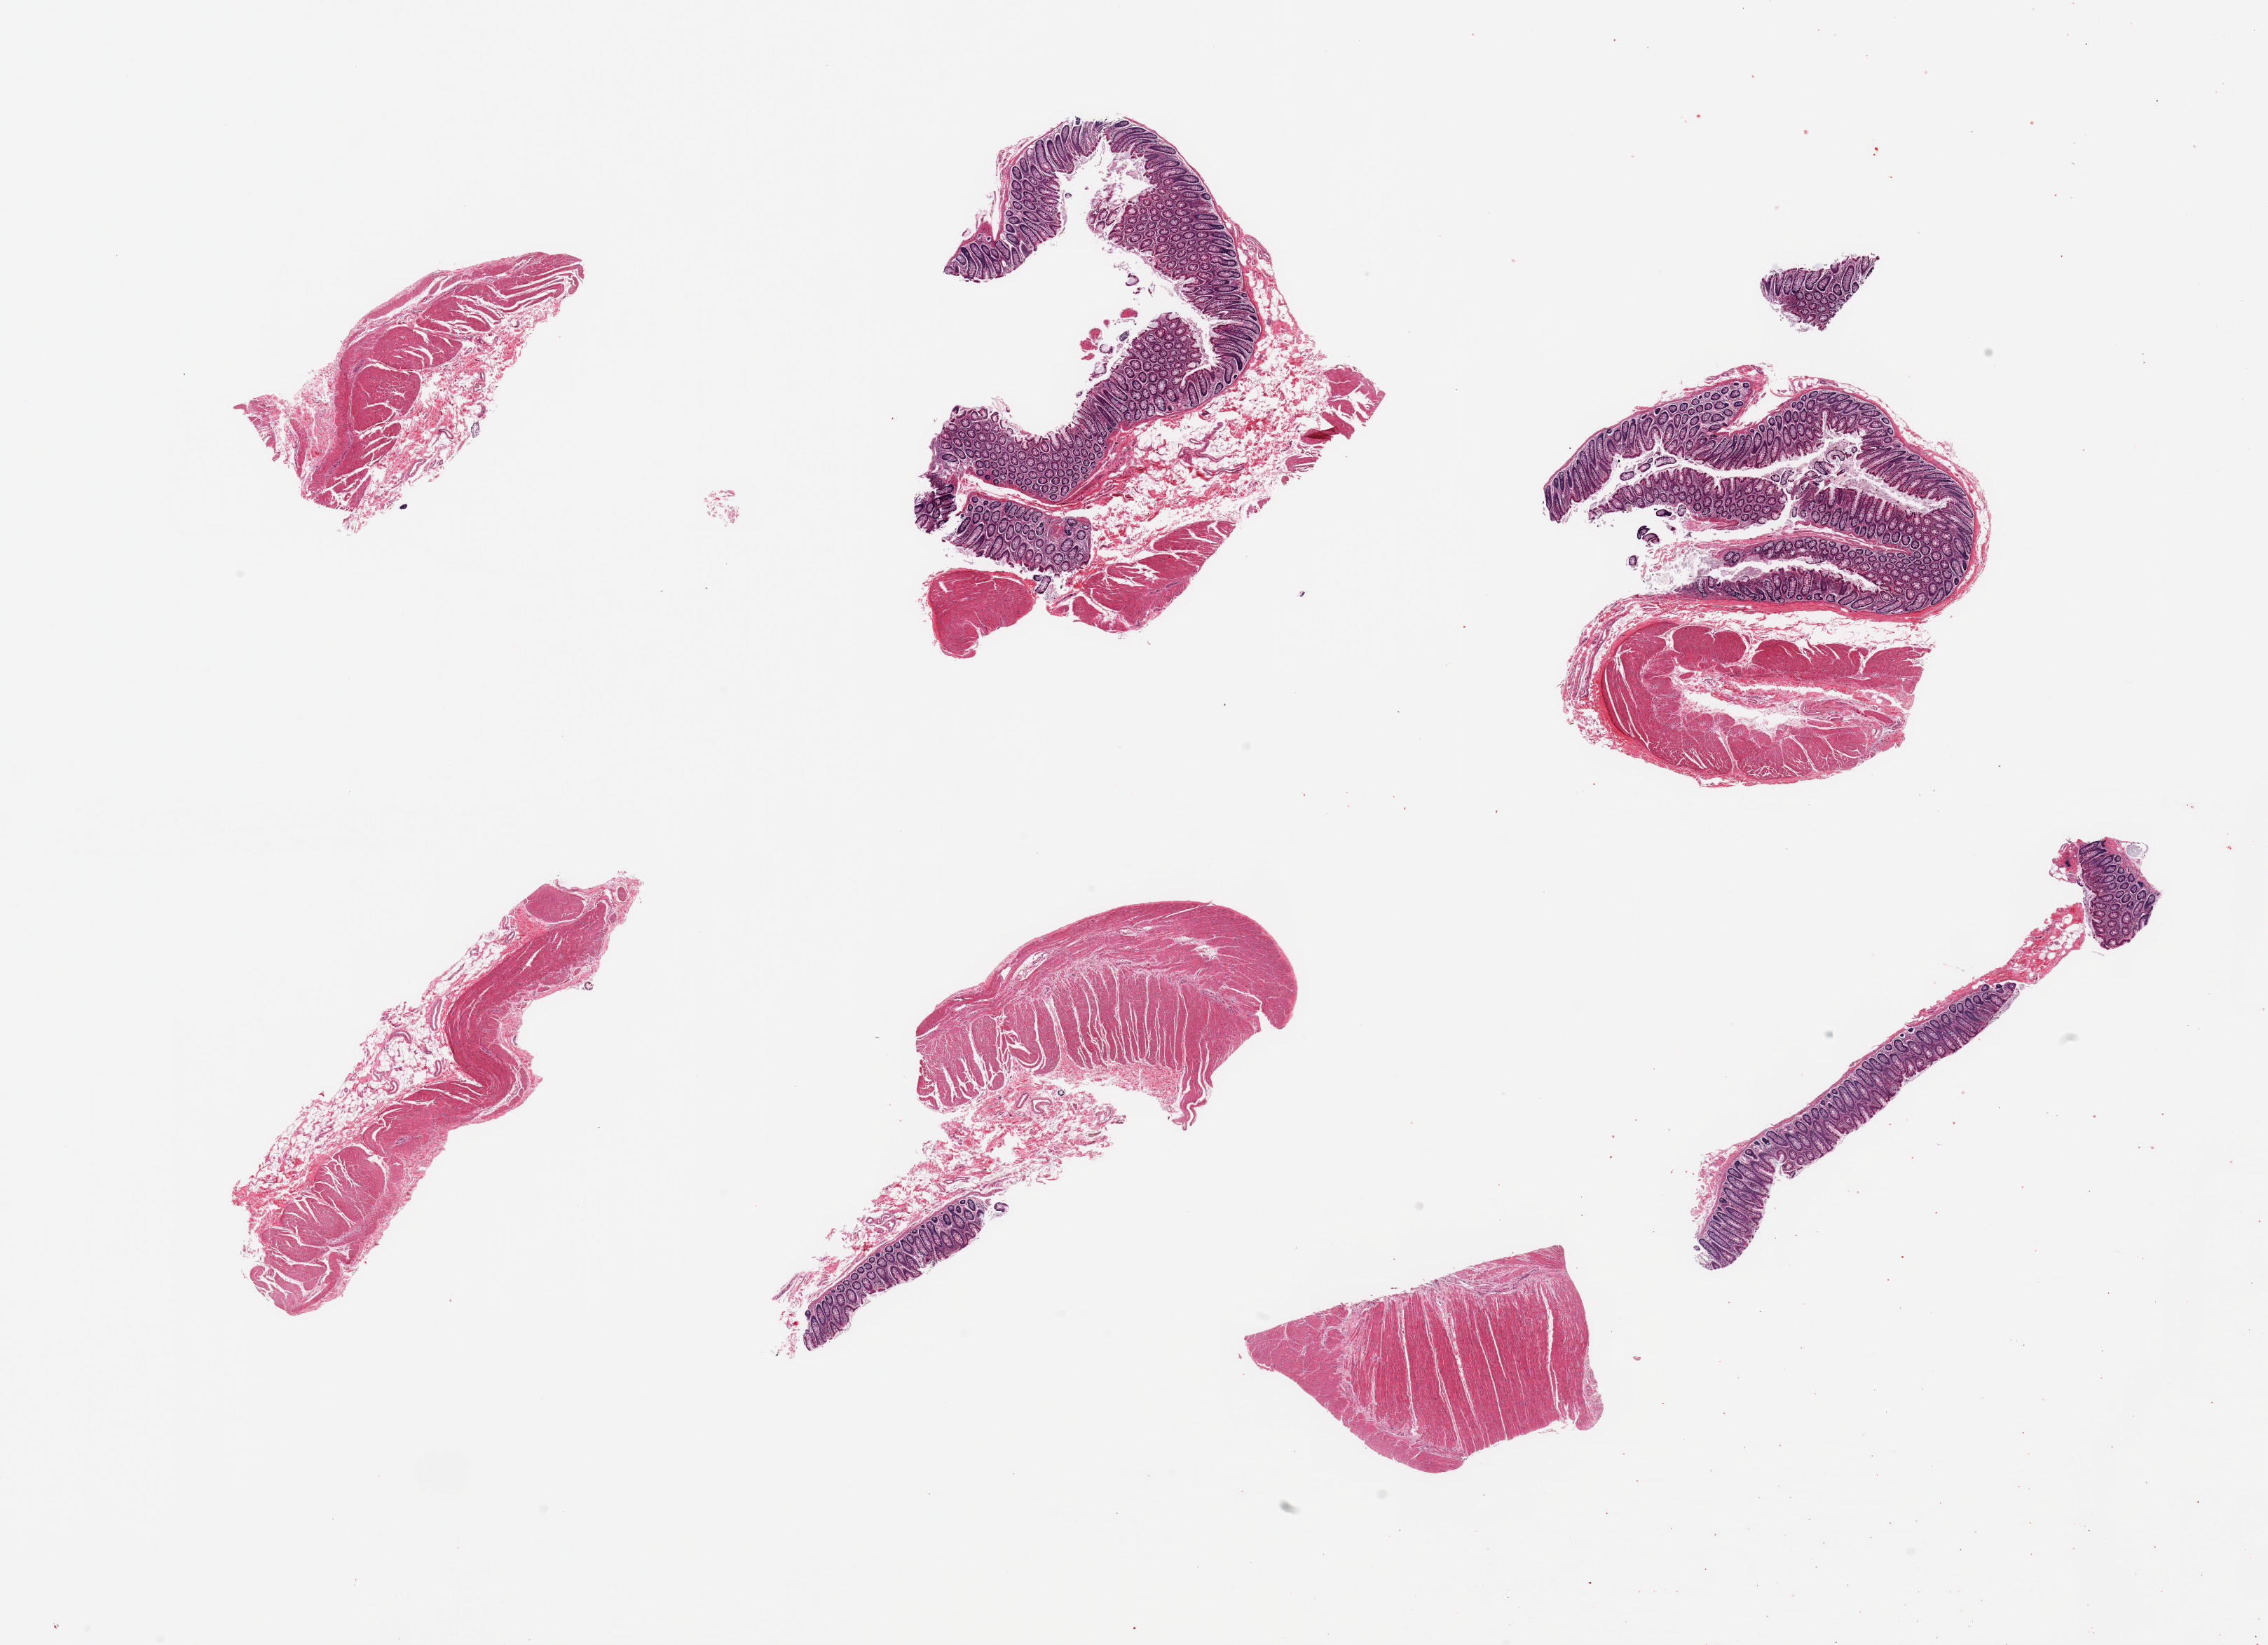
Digitized H&E-stained section, a low-resolution overview of the entire scanned area, about 25.6 x 18.6 mm (slide scanned at 20x); PAXgene-fixed paraffin-embedded (PFPE) section; sampled site (target tissue): transverse colon; tissue donor sample. Donor: male.
Reviewer comment on this tissue sample: 7 pieces; multiple pieces with variable composition (mucosa only, muscularis only, mucosa and muscularis).